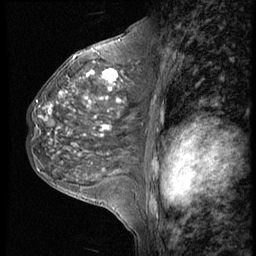
Breast MRI (dynamic contrast-enhanced), one sagittal slice; position 29 of 56 along the scan axis; 4 images stored at this slice position (order not interpretable as contrast timing); 1.5 T; TE 4.2 ms, TR 9 ms; 2.5 mm slice thickness; 256 × 256 image matrix, field of view 180 × 180 mm. Female patient, age 50 years. From the clinical record (not read from this slice): setting: breast cancer imaged before/during neoadjuvant chemotherapy; receptor status: triple-negative.
Annotated regions visible in this slice (semi-automatic segmentation, software-assisted and operator-edited):
- analysis volume of interest (the breast-tissue region the enhancement analysis was run in; not a lesion): box from (x=25, y=46) to (x=148, y=188) px
- tumour enhancement mask (voxels above the 140 % enhancement threshold inside the analysis volume of interest): (x=40, y=70)–(x=120, y=135)